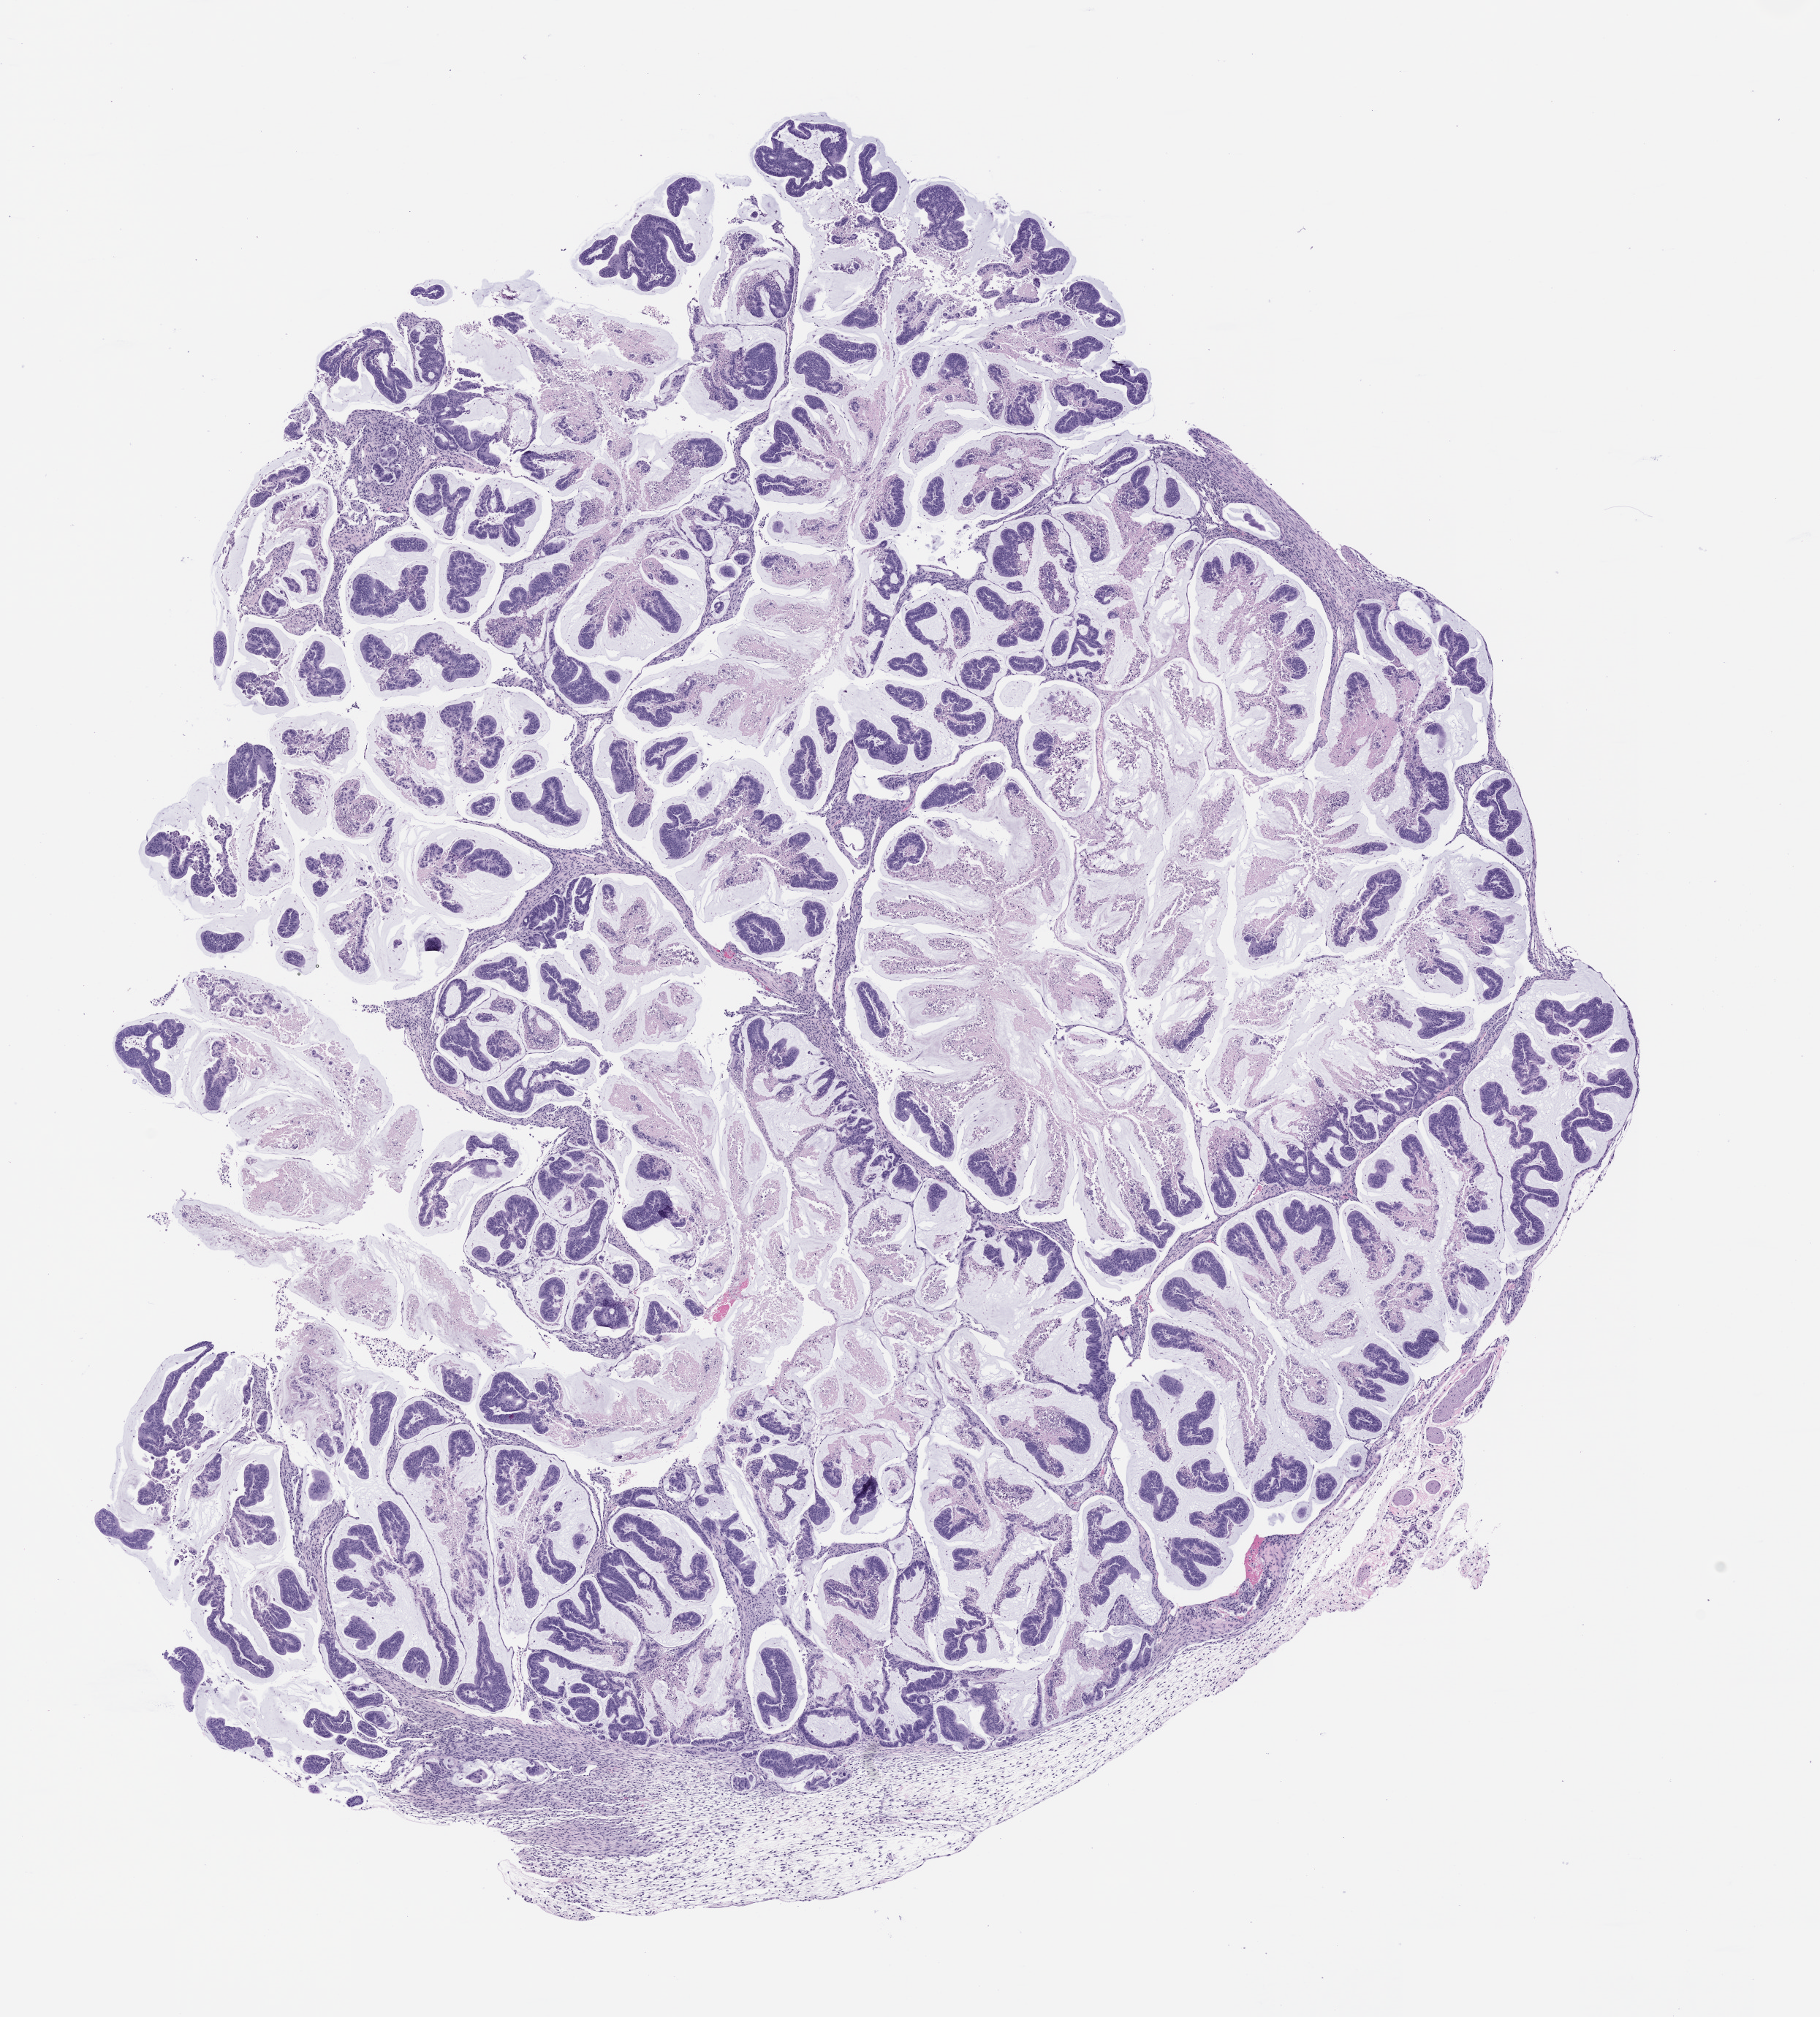
Whole-slide image, hematoxylin and eosin (H&E): patient-derived xenograft (human tumor grown in a mouse), passage 0 — a low-resolution overview of the entire scanned area, about 10.0 x 11.1 mm. Formalin-fixed paraffin-embedded section. Tumor site category: colon.
* originating patient diagnosis: Colon Adenocarcinoma